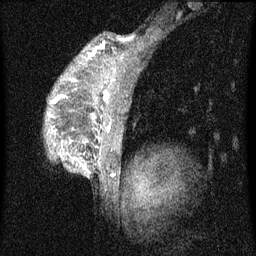
Breast MRI (dynamic contrast-enhanced), one sagittal slice; position 52 of 60 along the scan axis; dynamic contrast-enhanced series, image 2 of 4 at this slice position (ordered by acquisition); 1.5 T; TE 4.2 ms, TR 8 ms; 256 × 256 image matrix, field of view 180 × 180 mm. Female patient, age 50 years.
Structures marked on this image (semi-automatically segmented with operator editing):
- analysis volume of interest (the breast-tissue region the enhancement analysis was run in; not a lesion): box from (x=46, y=48) to (x=124, y=177) px
- tumour enhancement mask (voxels above the 70 % enhancement threshold inside the analysis volume of interest): (x=60, y=96)–(x=110, y=167)